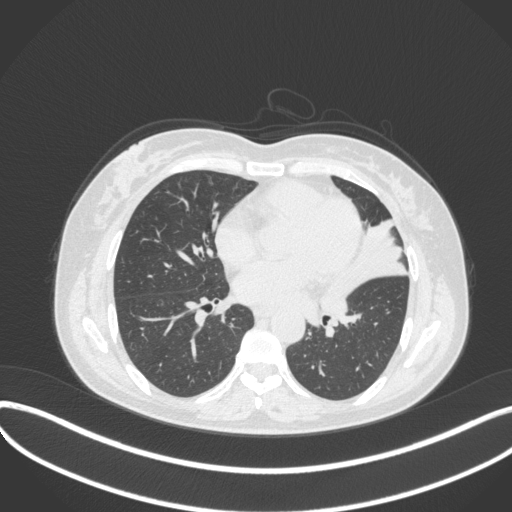
Chest CT, one axial slice. Position 163 of 373 along the scan axis. Reconstruction kernel B31f. 120 kVp. Lung window (W 1500 / L -600 HU). 1 mm slice thickness. 512 × 512 image matrix, field of view 400 × 400 mm. Patient: female, 54 years. Case-level facts recorded for this patient, not image findings: clinical TNM (as recorded): T2a N1 M0; histopathological grade: G3.
Structures marked on this image (bounding box drawn by a radiologist):
- lung tumour (recorded histology: small cell carcinoma): box from (x=312, y=271) to (x=363, y=321) px